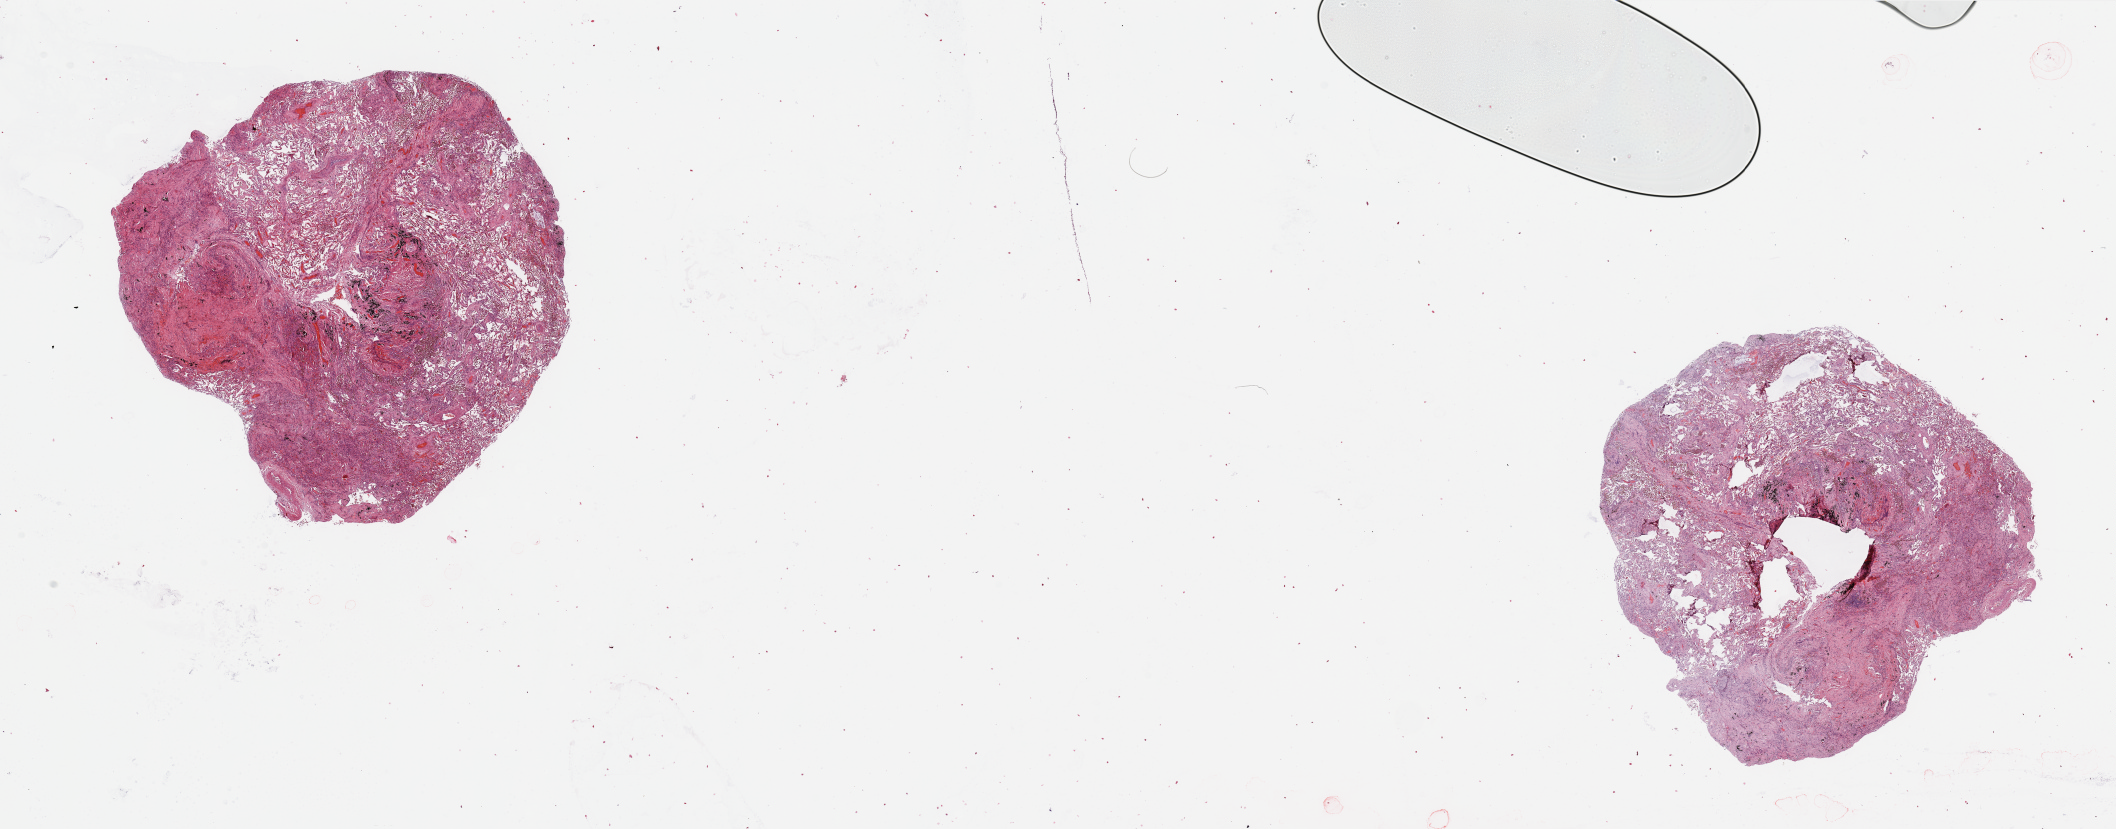
Digitized H&E tissue section (whole slide), low-resolution overview of the scanned area, about 33.5 x 13.1 mm (from a 20x scan). Lung, normal (non-tumour) tissue. Patient: male, age 53 years.
This section: normal (non-tumour) tissue from the same patient. Patient diagnosis: Squamous cell carcinoma, NOS.